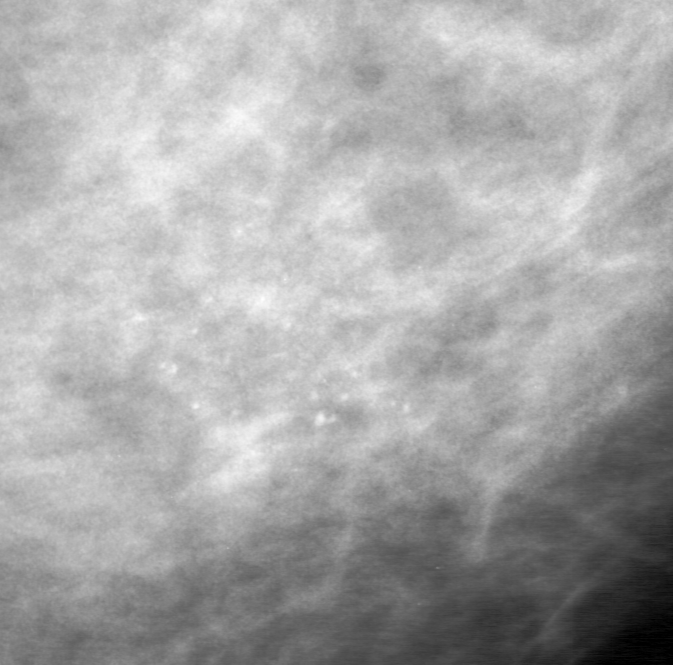
Cropped region of a digitized screen-film mammogram centred on a radiologist-marked abnormality, left breast, CC view.
- Marked abnormality: calcifications, morphology pleomorphic, distribution clustered; BI-RADS assessment category 0; subtlety rating 4 on a 1 (subtle) to 5 (obvious) scale; pathology result (as recorded, not read from the image): malignant.